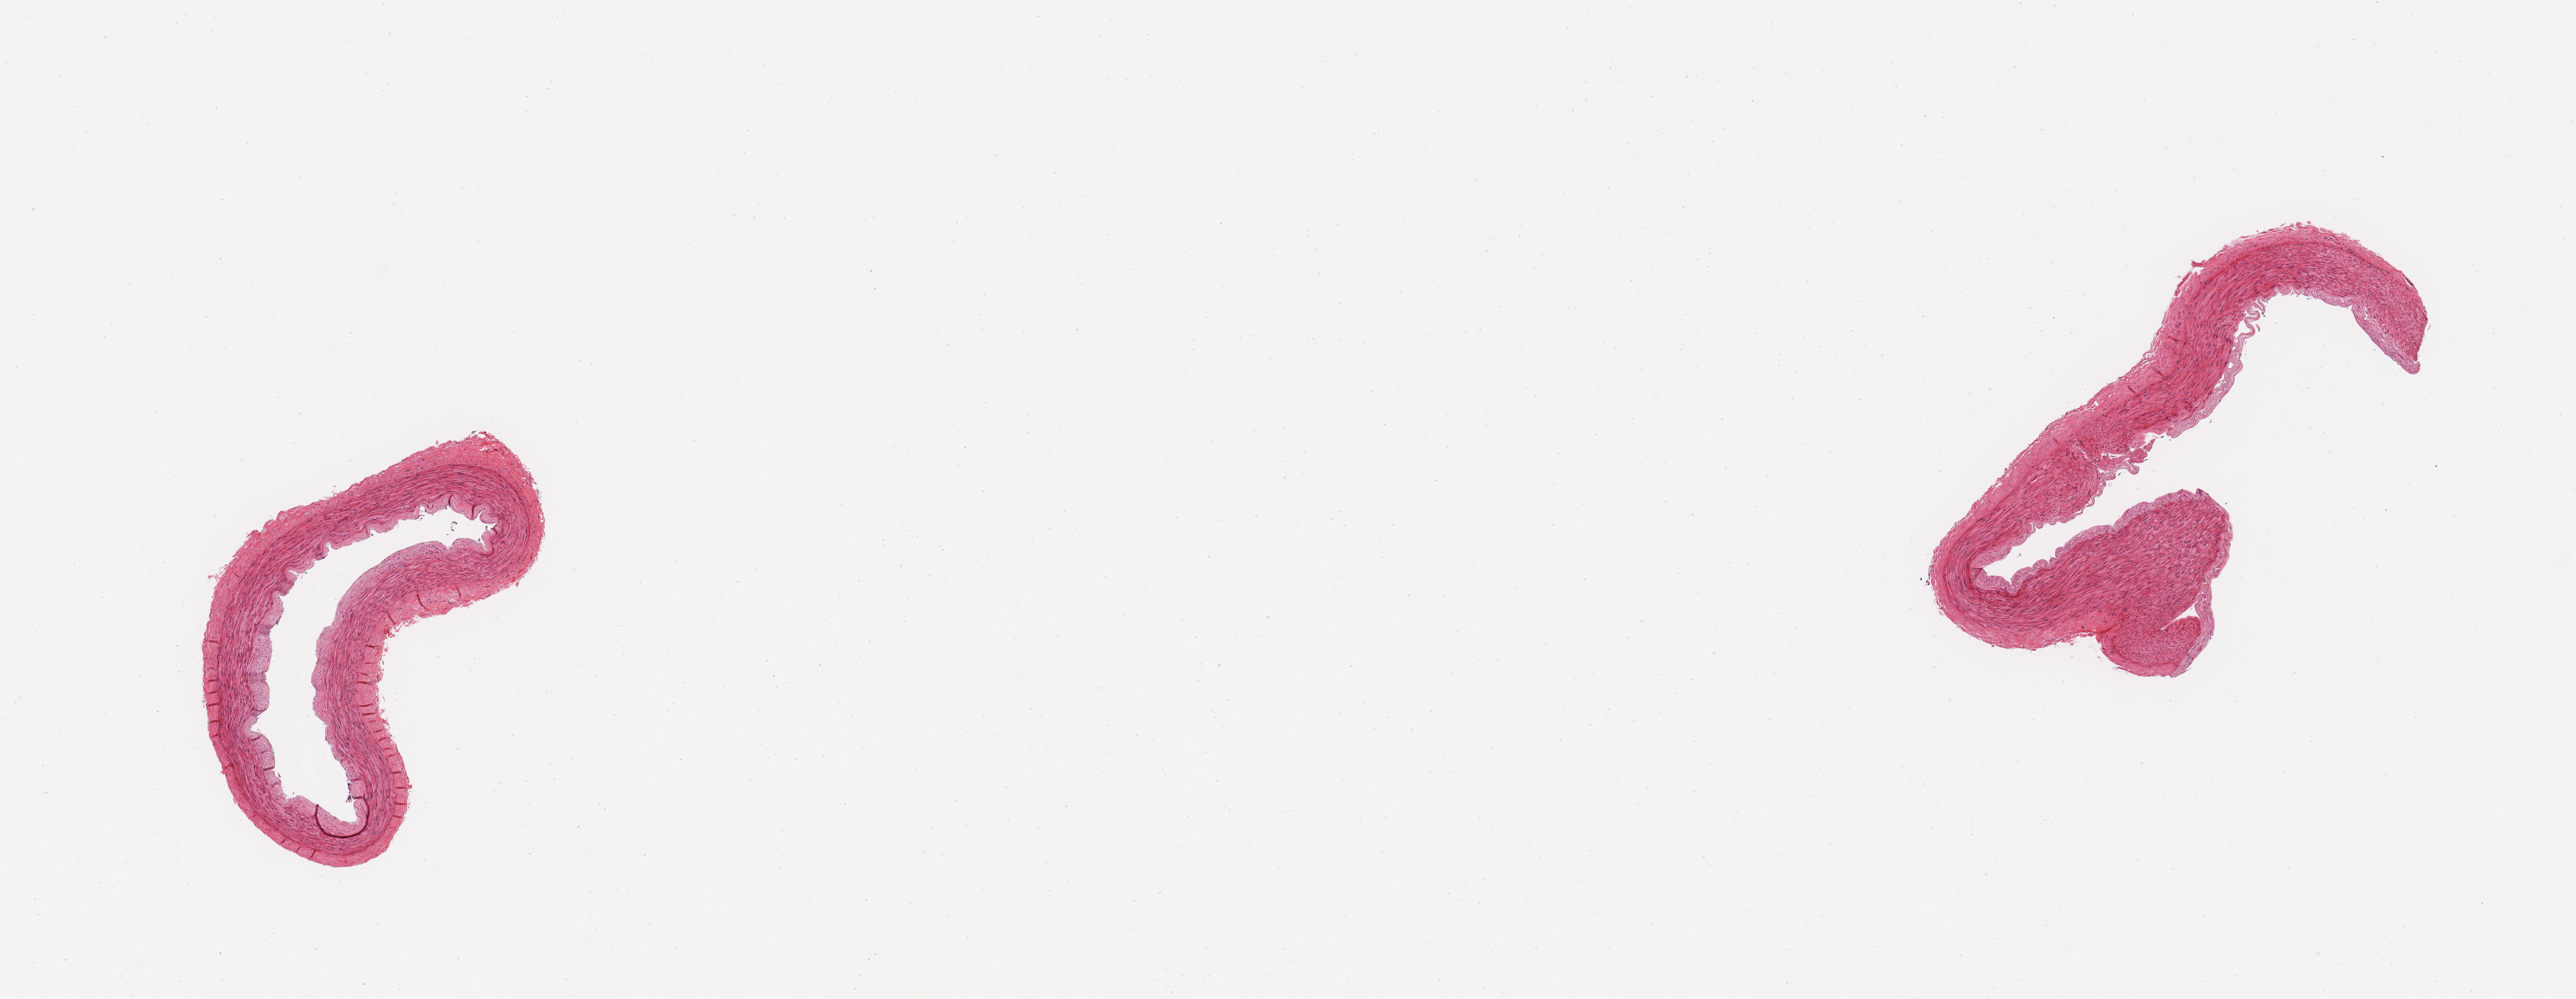
H&E whole-slide image, brightfield — low-resolution overview of the scanned area, about 13.8 x 5.3 mm (acquisition: 20x scan). PAXgene-fixed, paraffin-embedded tissue. Section of tibial artery (target tissue). Tissue donor sample.
Reviewer comment on this tissue sample: 2 pieces; minimal plaque; well trimmed.